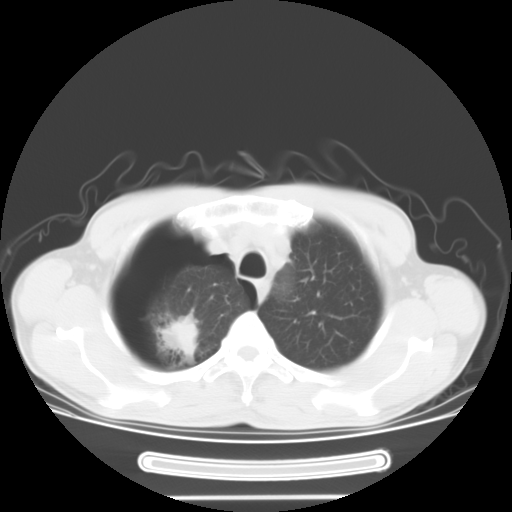
Chest CT, one axial slice; position 28 of 34 along the scan axis; reconstruction kernel STANDARD; 120 kVp; lung window (W 1500 / L -600 HU); 10 mm slice thickness; 512 × 512 image matrix, field of view 375 × 375 mm. Male patient. From the clinical record (not read from this slice): clinical TNM (as recorded): T1c N0 M0.
Annotated regions visible in this slice (bounding box drawn by a radiologist):
- lung tumour (recorded histology: adenocarcinoma): bounding box (x1, y1, x2, y2) in pixels: (159, 314, 199, 360)